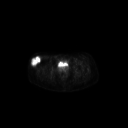
FDG PET of an extremity soft-tissue mass (from a PET/CT study), one axial slice; slice 63 of 267 in the series (ordered by position); 3.27 mm slice thickness; 128 × 128 image matrix, field of view 700 × 700 mm. Patient: female, 34 years. From the clinical record (not read from this slice): histological type: synovial sarcoma; grade: intermediate; site of the primary tumour: right thigh.
Outlined on this slice (expert contour drawn on MRI and transferred to this co-registered scan by the dataset authors):
- gross tumour volume including surrounding oedema: box from (x=30, y=56) to (x=41, y=67) px
- gross tumour volume (mass): (x=30, y=56)–(x=41, y=67)